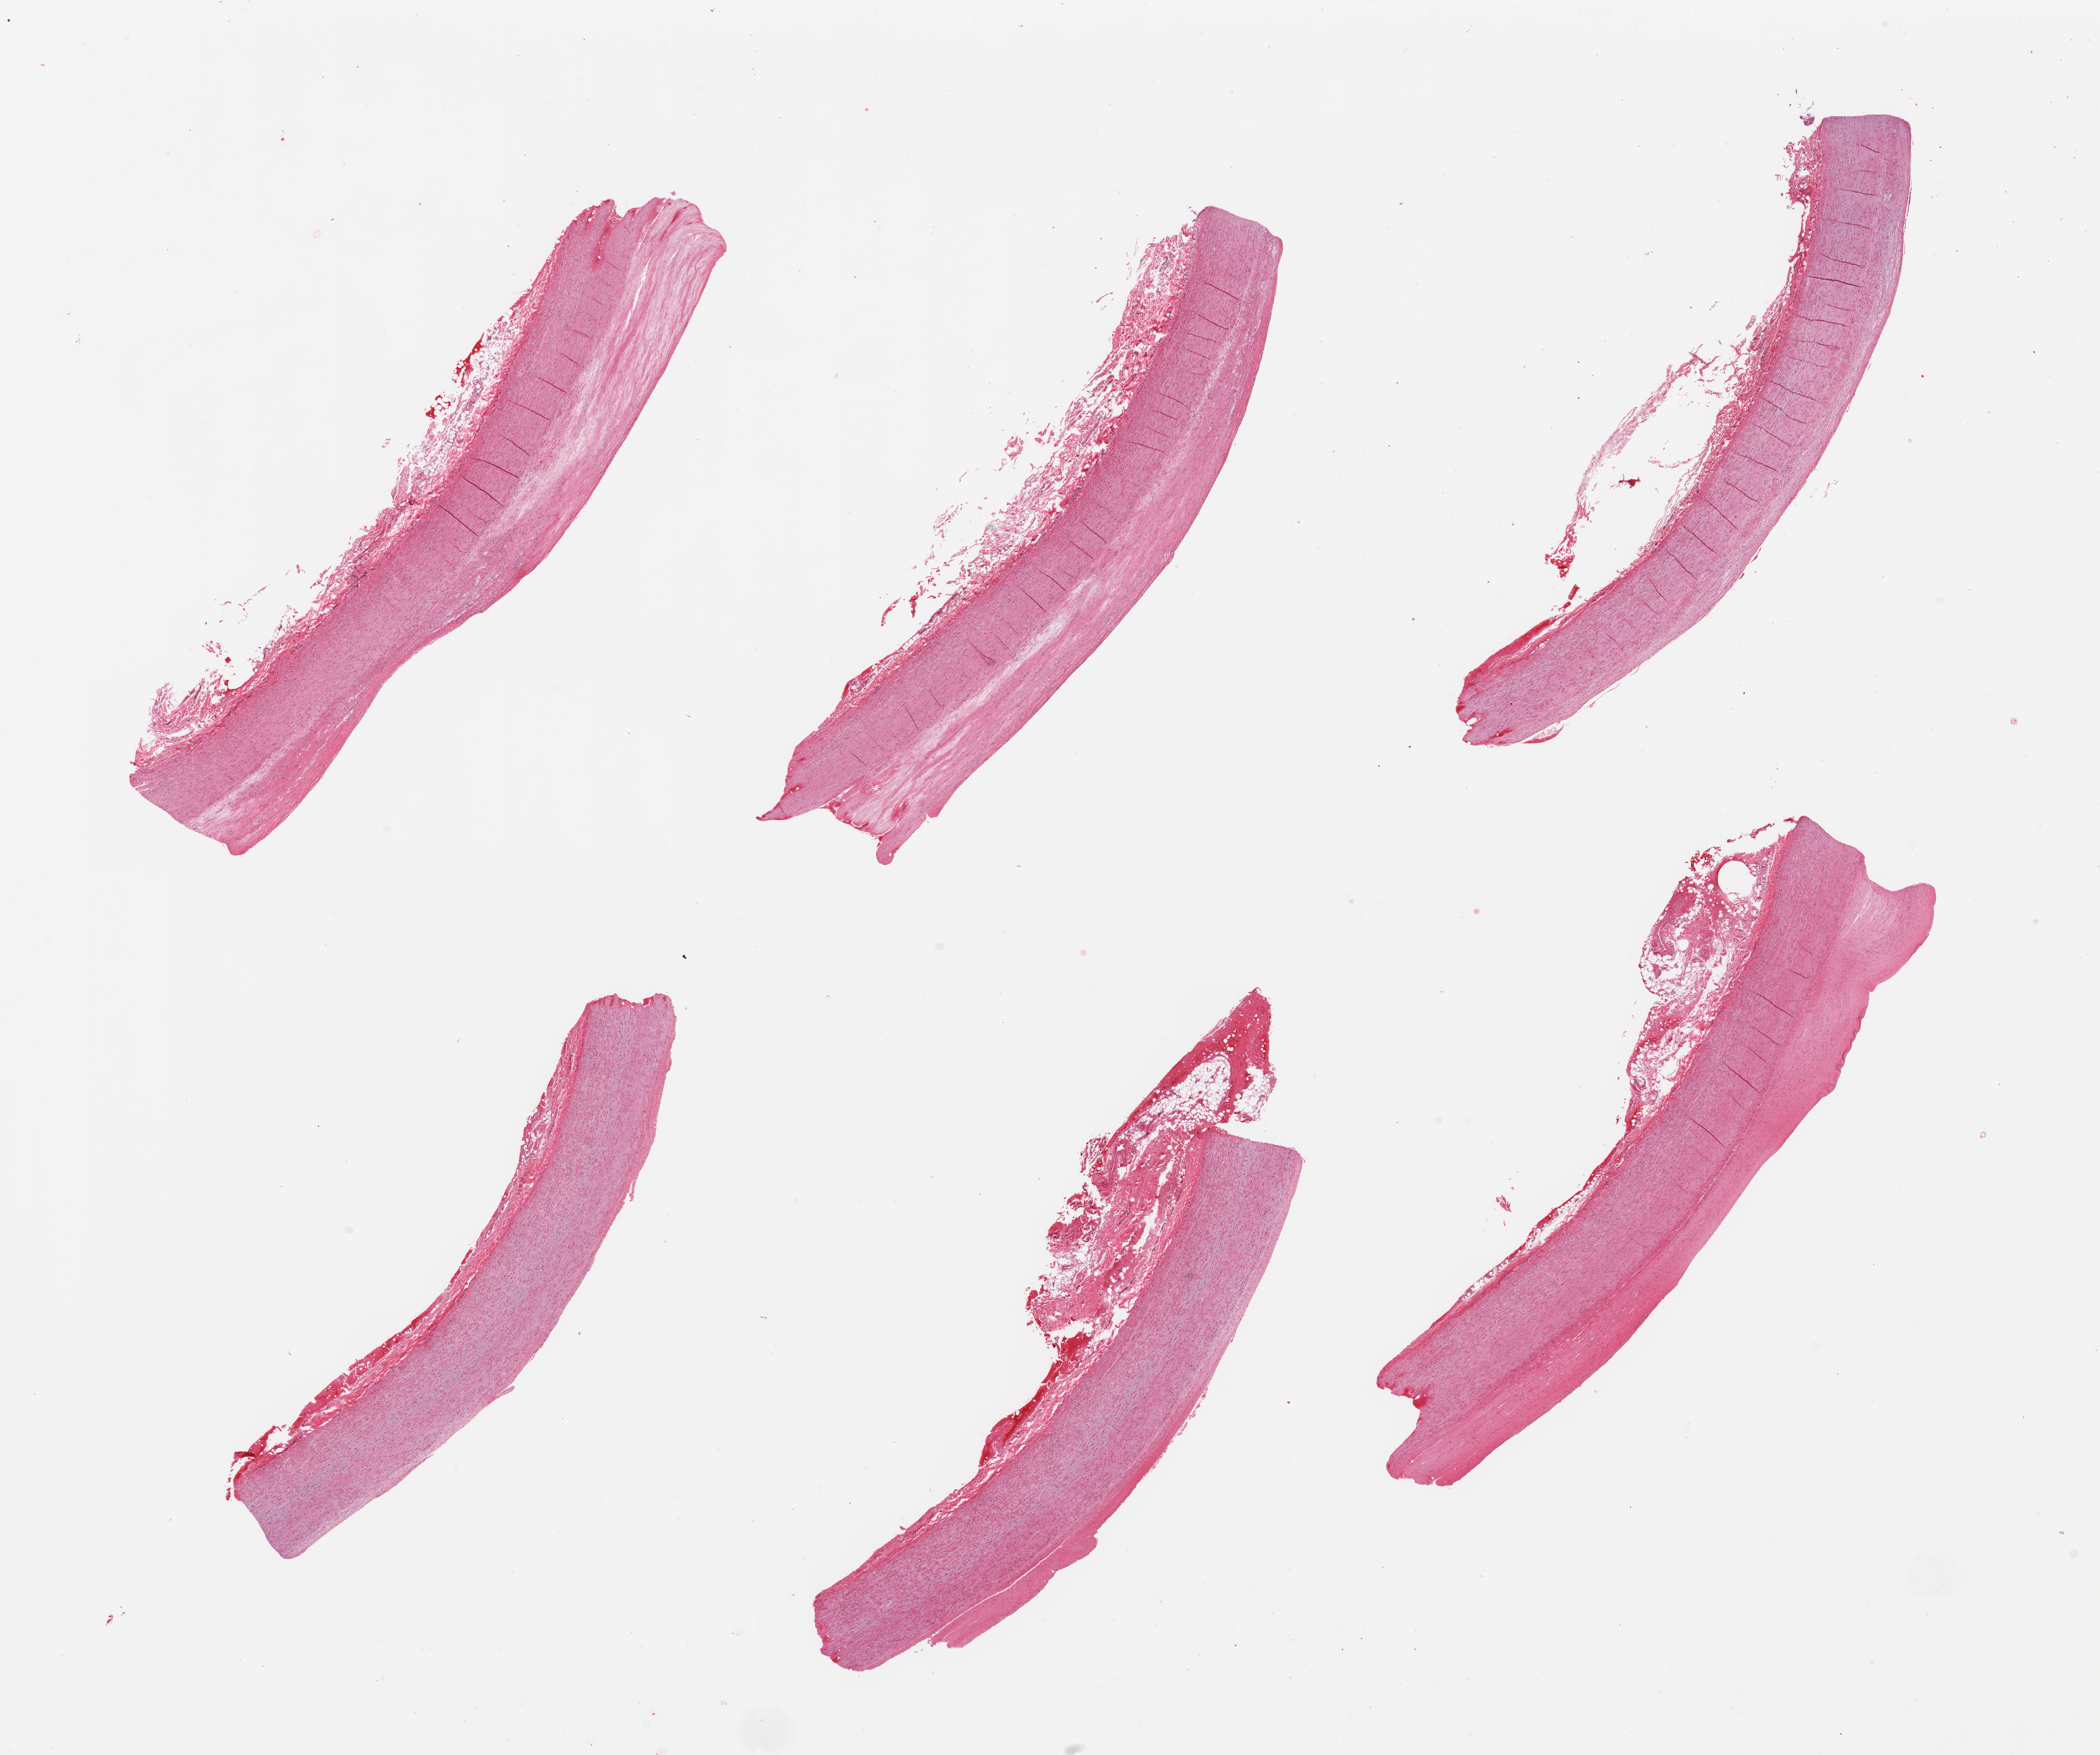
H&E whole-slide image — a low-resolution overview of the entire scanned area, about 24.6 x 20.6 mm (from a 20x scan); PAXgene-fixed, paraffin-embedded tissue; sampled site (target tissue): aorta; tissue donor sample. Female donor.
Pathologist's review note for this sample: 6 pieces; atherosclerosis.